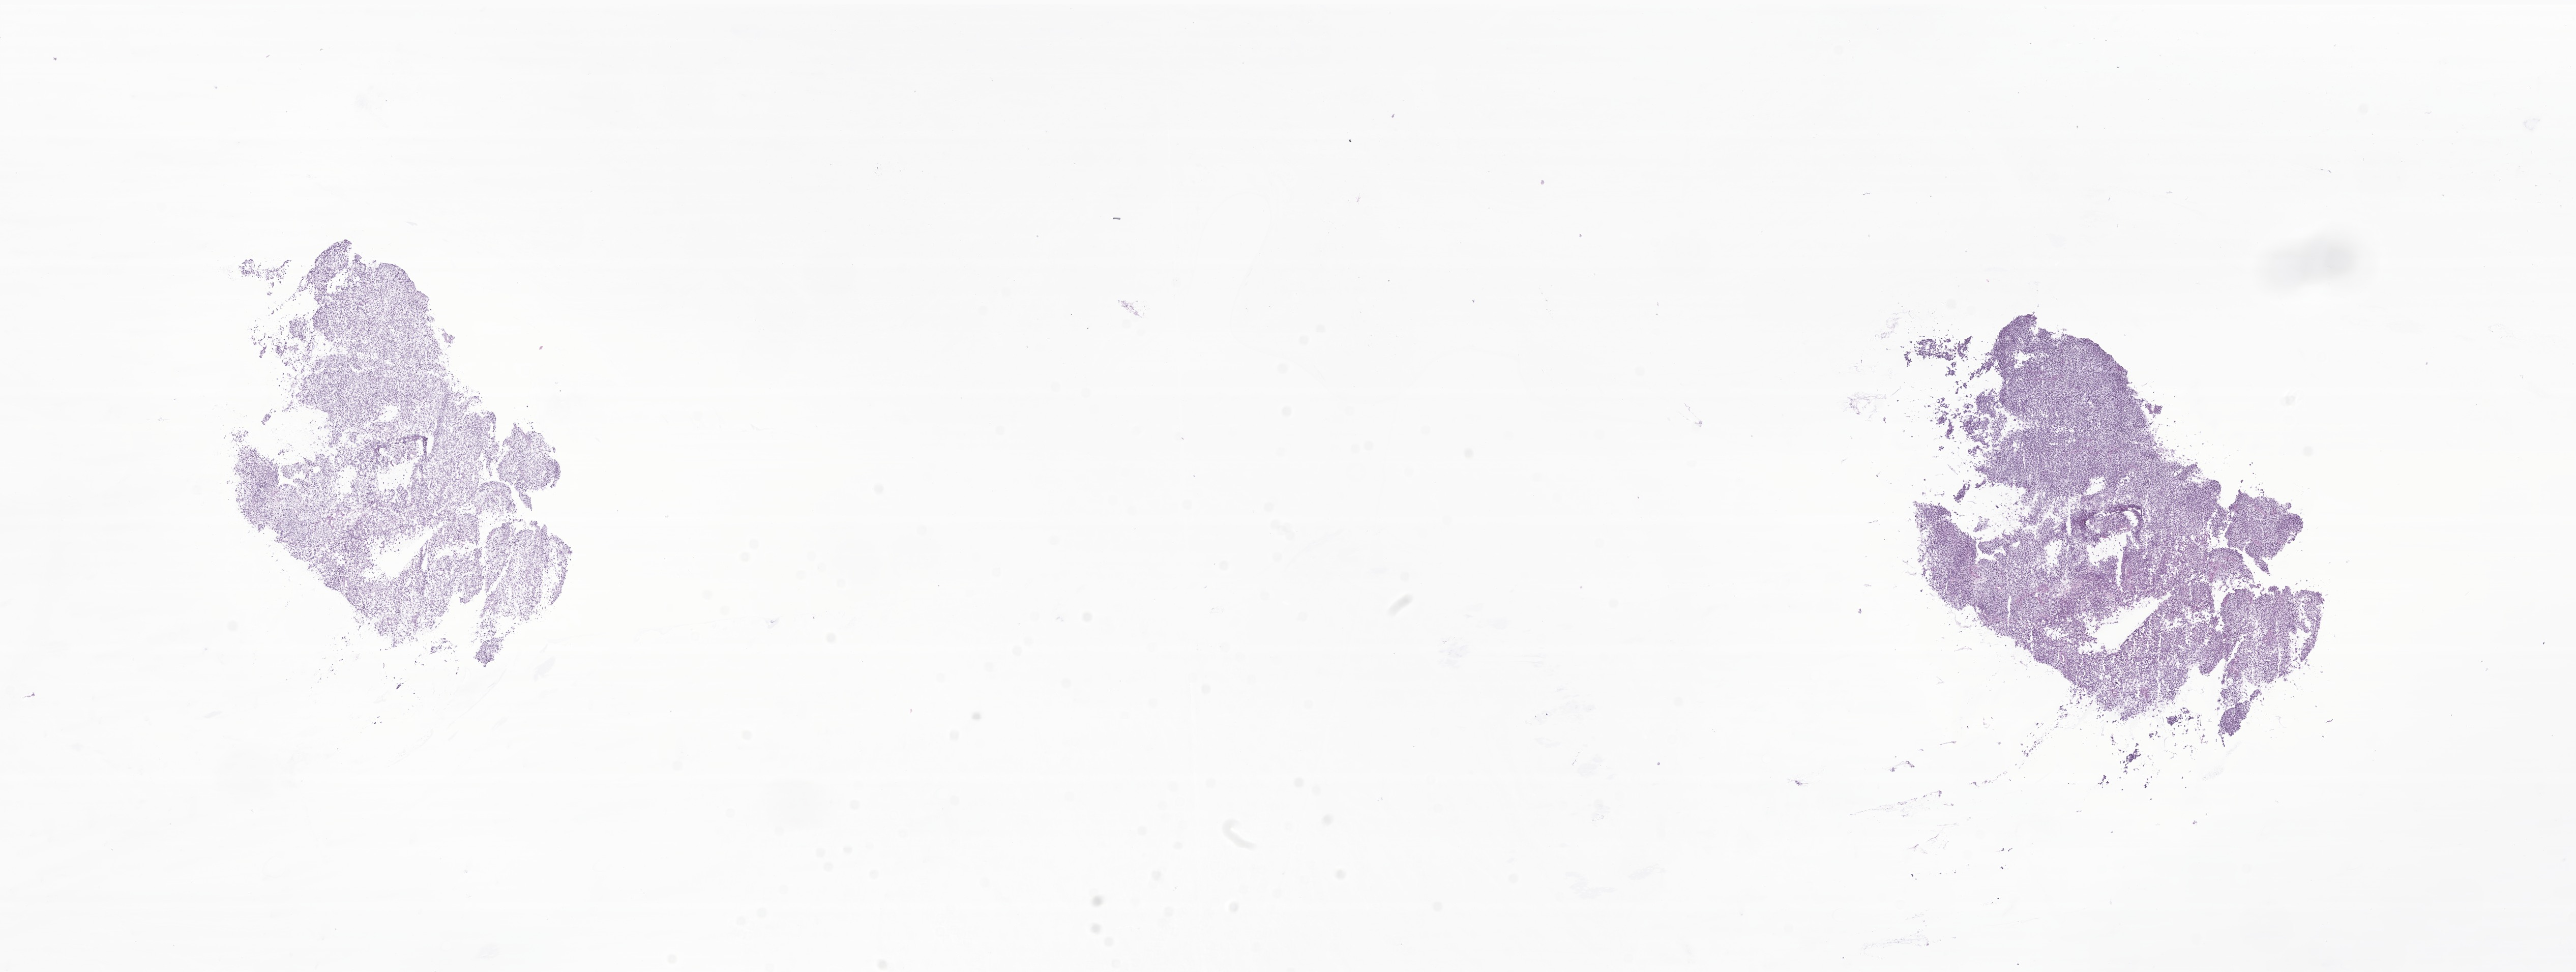
Digitized hematoxylin and eosin (H&E)-stained section of tumor tissue from the orbit, low-resolution overview of the scanned area, about 21.4 x 8.1 mm; frozen section. Male patient, age 118 months (9 years 10 months).
Recorded diagnosis: Rhabdomyosarcoma, NOS.